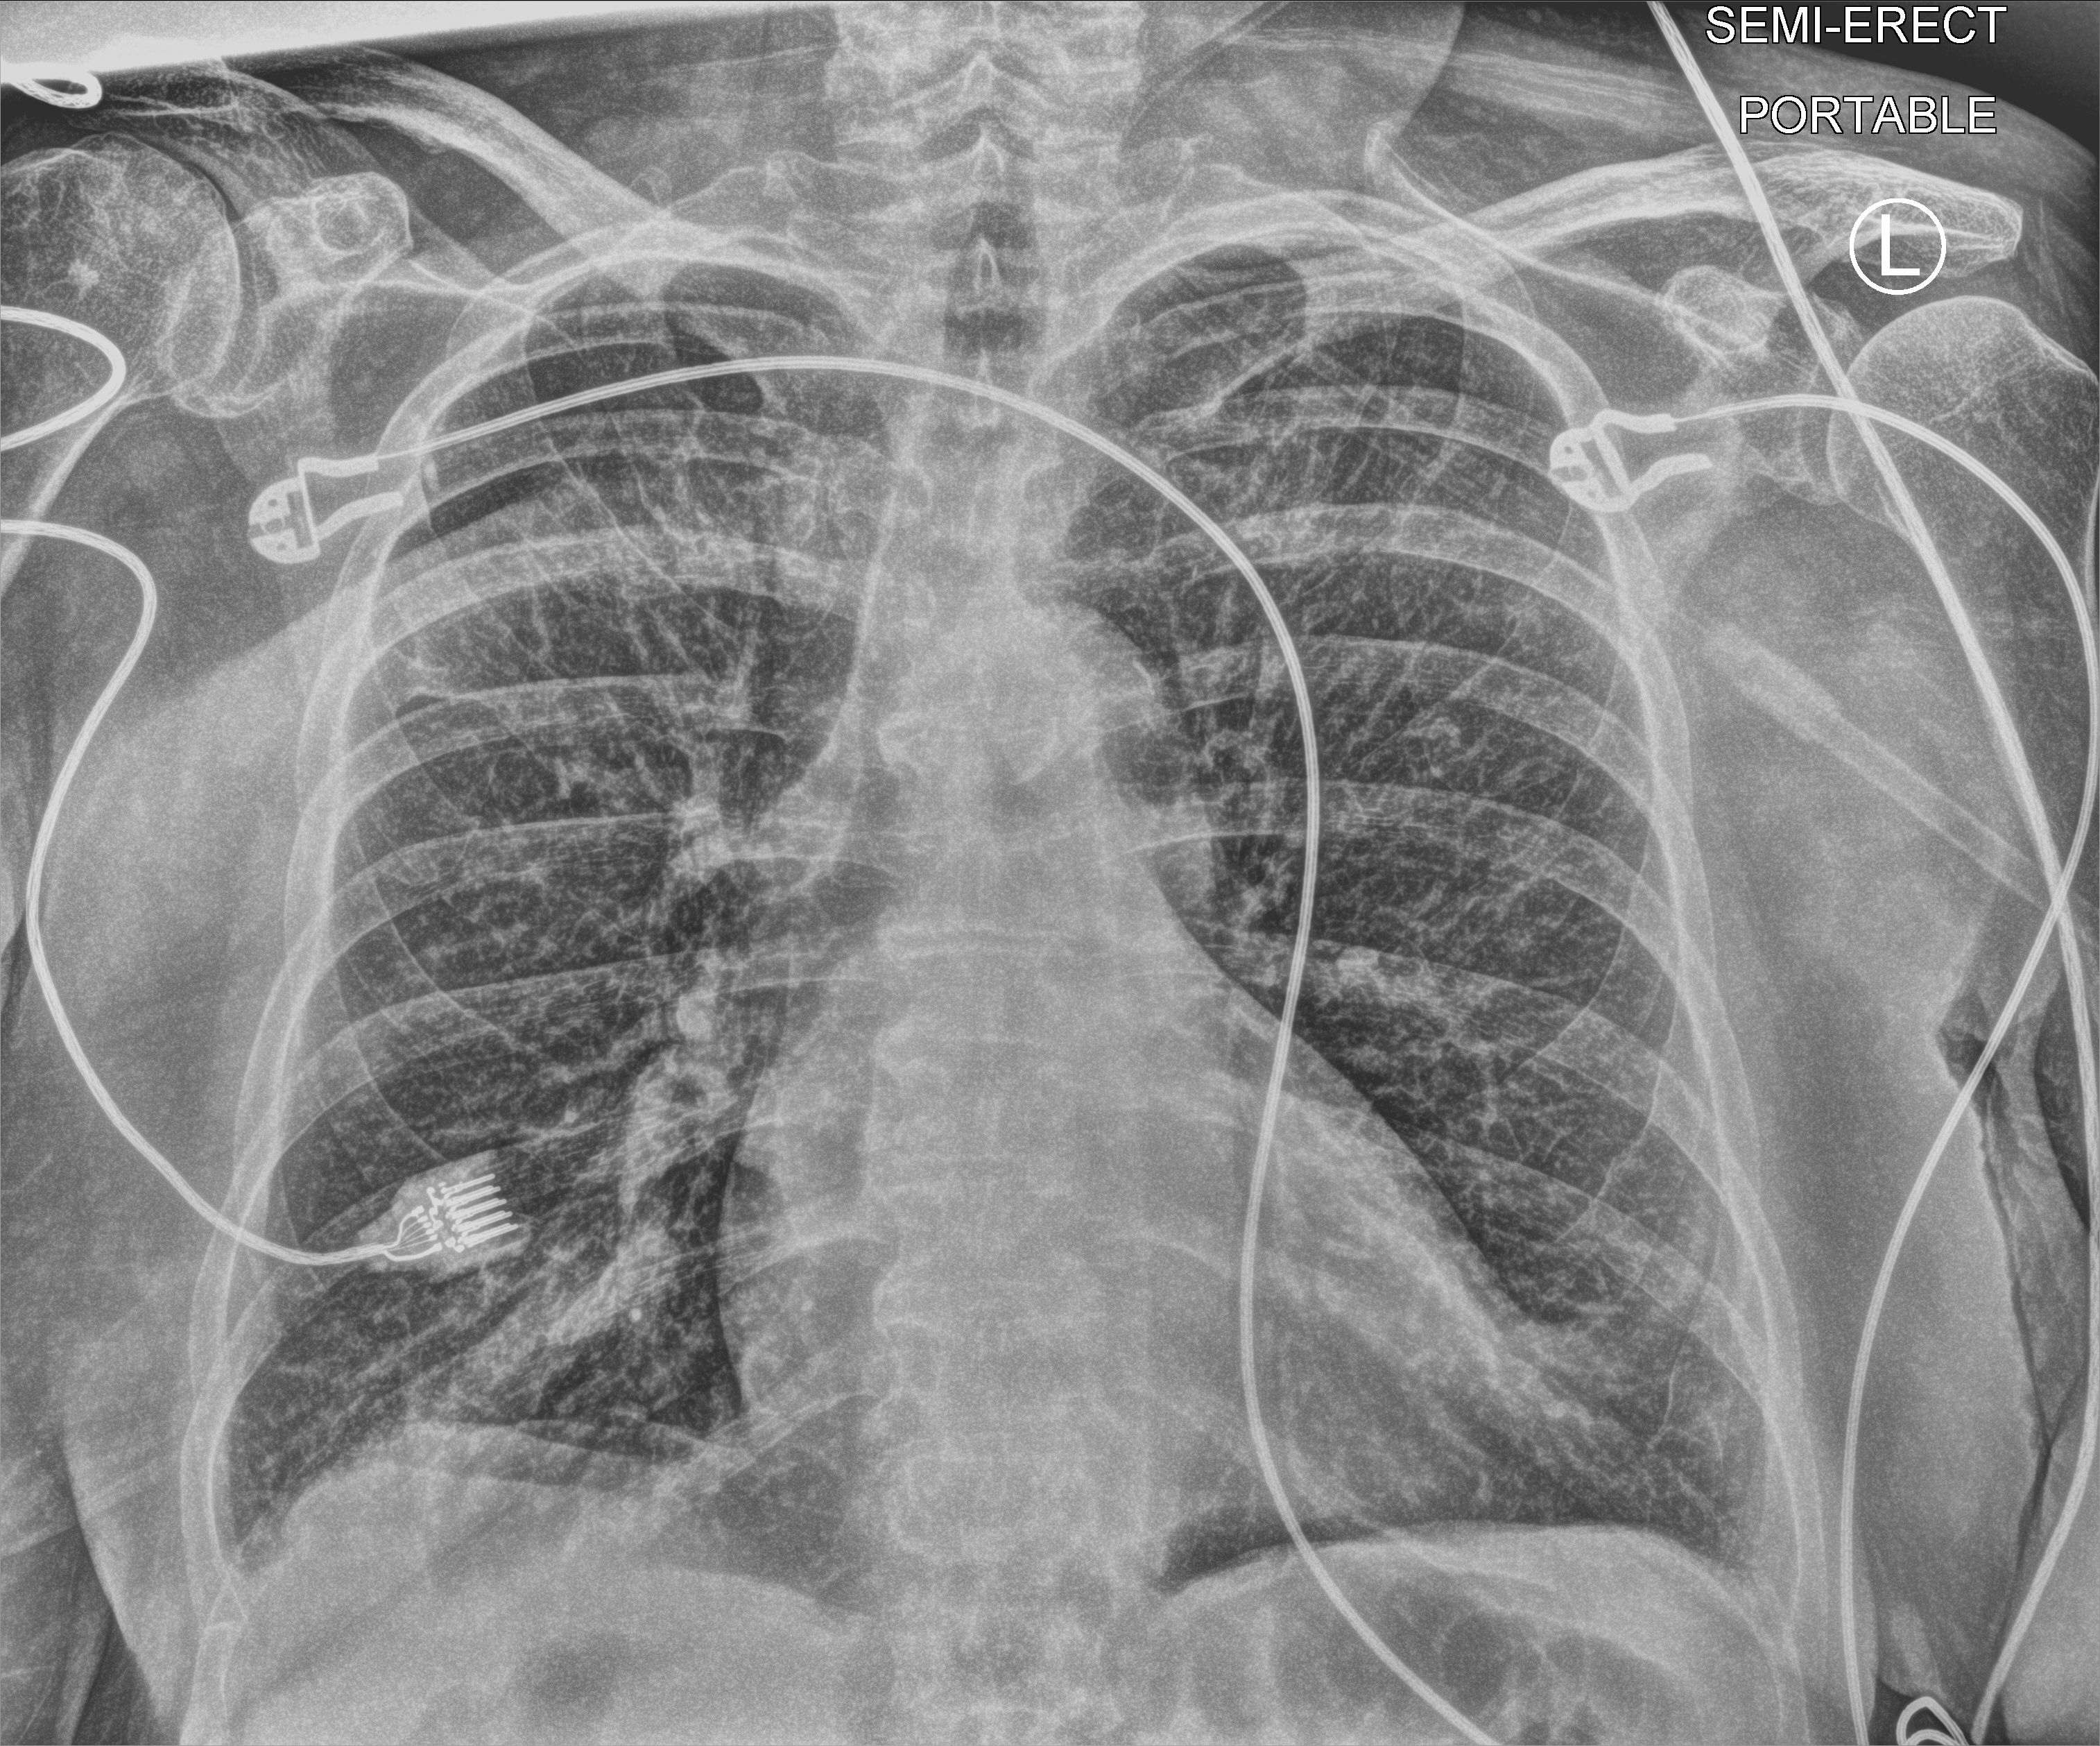
Portable chest radiograph; anteroposterior (AP) projection. Female patient hospitalised with COVID-19, age 75–90 years.
From the hospital-stay record, not from the radiograph (when in the stay this image was taken is not recorded): admitted to intensive care during this hospital stay: no.